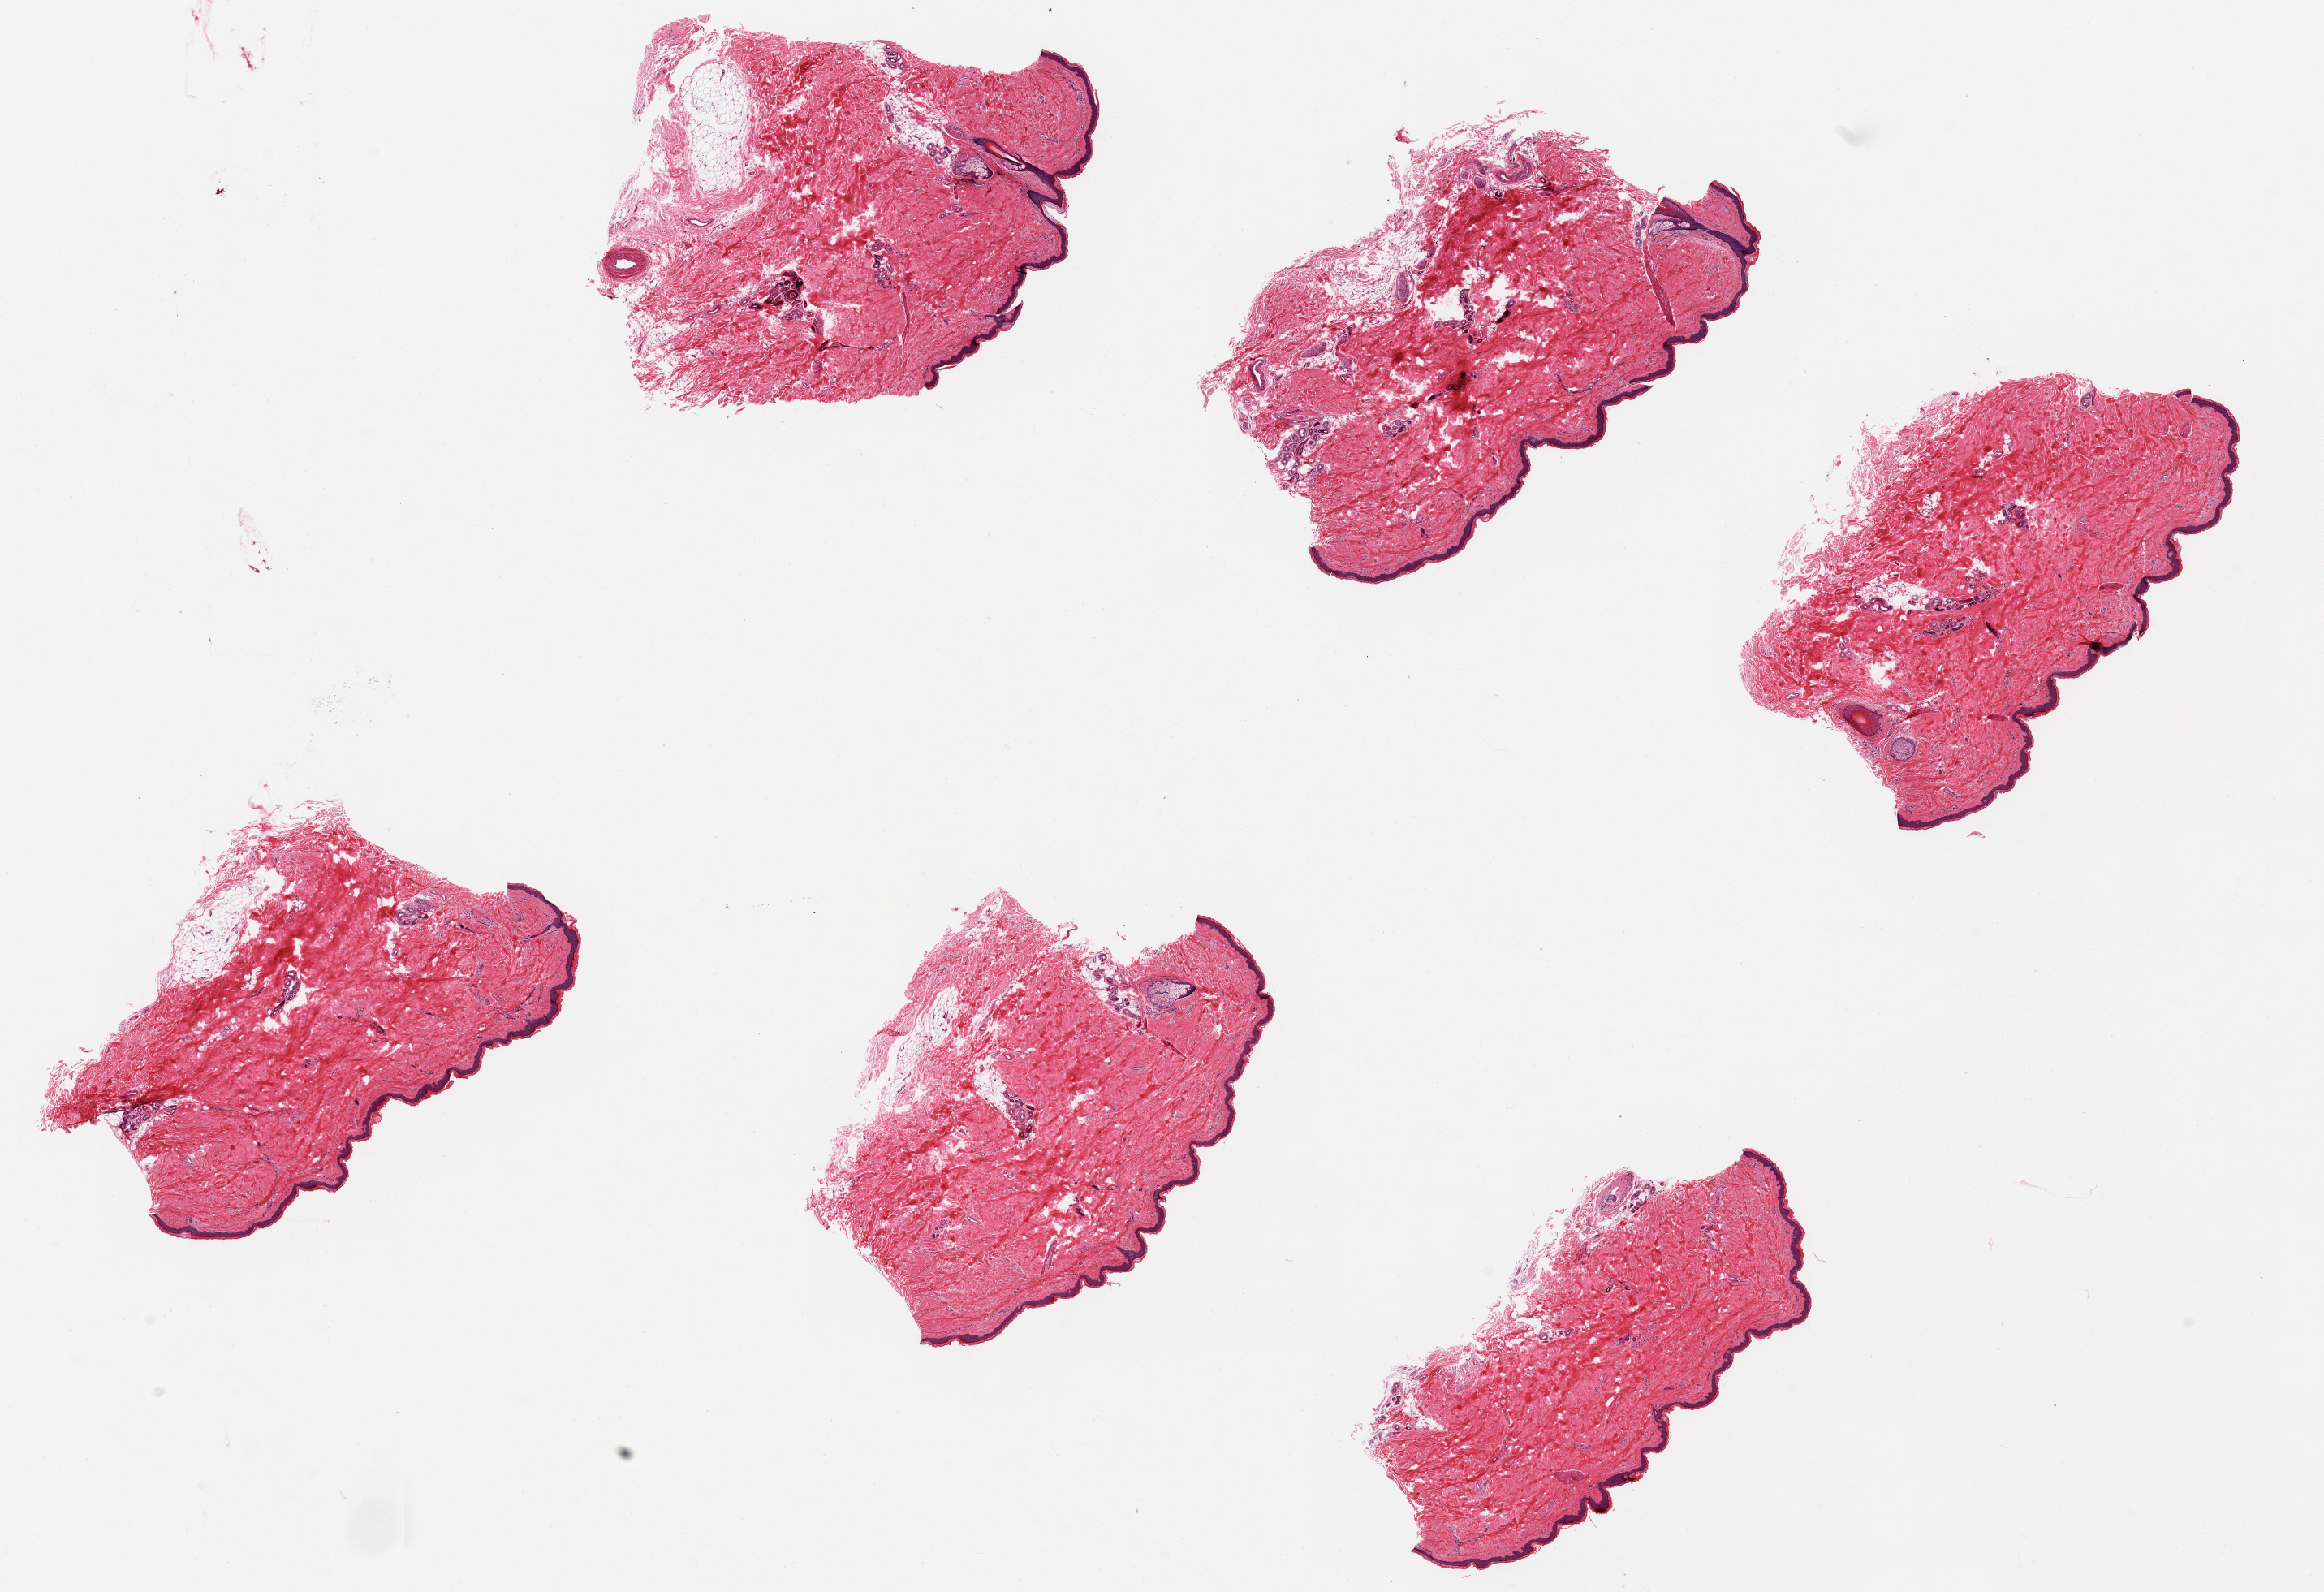
Whole-slide image, haematoxylin and eosin stain, a low-resolution overview of the entire scanned area, about 22.6 x 15.5 mm (from a 20x scan), PAXgene-fixed paraffin-embedded (PFPE) section, section of skin of lower leg (target tissue), tissue donor sample.
* reviewer comment on this tissue sample: 6 pieces, up to ~5 x 3.8 mm; epidermis ~90um